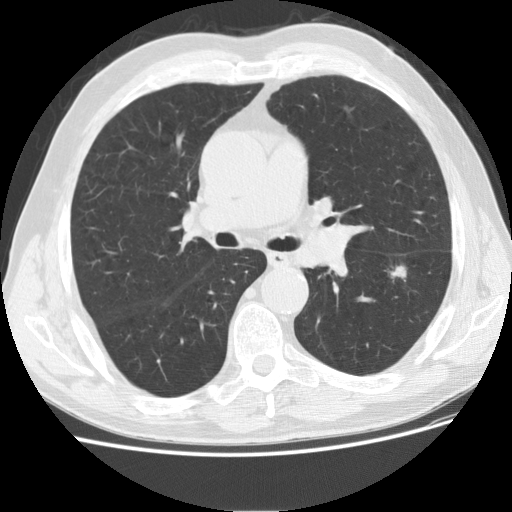
Low-dose screening chest CT, one axial slice. Slice 109 of 175 in the series (ordered by position). Reconstruction kernel STANDARD. 120 kVp. Lung window (W 1500 / L -600 HU). 2.5 mm slice thickness. 512 × 512 image matrix, field of view 360 × 360 mm.
Structures marked on this image (outlined manually by an expert reader):
- lesion 1 (tumor, lower lobe of left lung): bounding box [x1, y1, x2, y2] px = [390, 266, 407, 279]